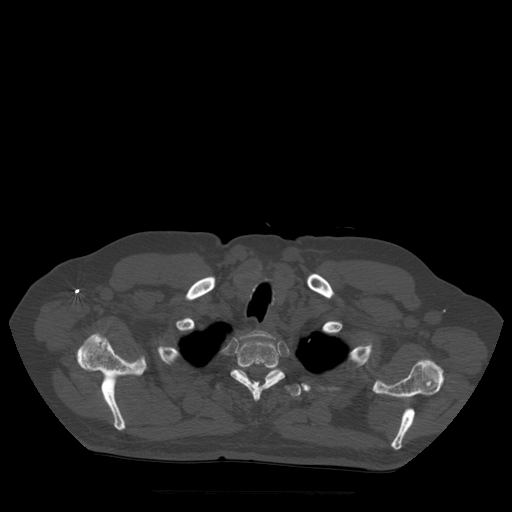
CT including the spine, one axial slice; slice 423 of 522 in the series (ordered by position); bone window (W 1800 / L 400 HU); 512 × 512 image matrix. Patient age 72 years. Case-level facts recorded for this patient, not image findings: primary cancer: prostate.
Outlined on this slice (semi-automatically segmented with operator editing):
- T1 vertebra: box from (x=241, y=331) to (x=273, y=339) px
- T2 vertebra: (x=231, y=336)–(x=285, y=400)
- T3 vertebra: (x=216, y=367)–(x=302, y=397)